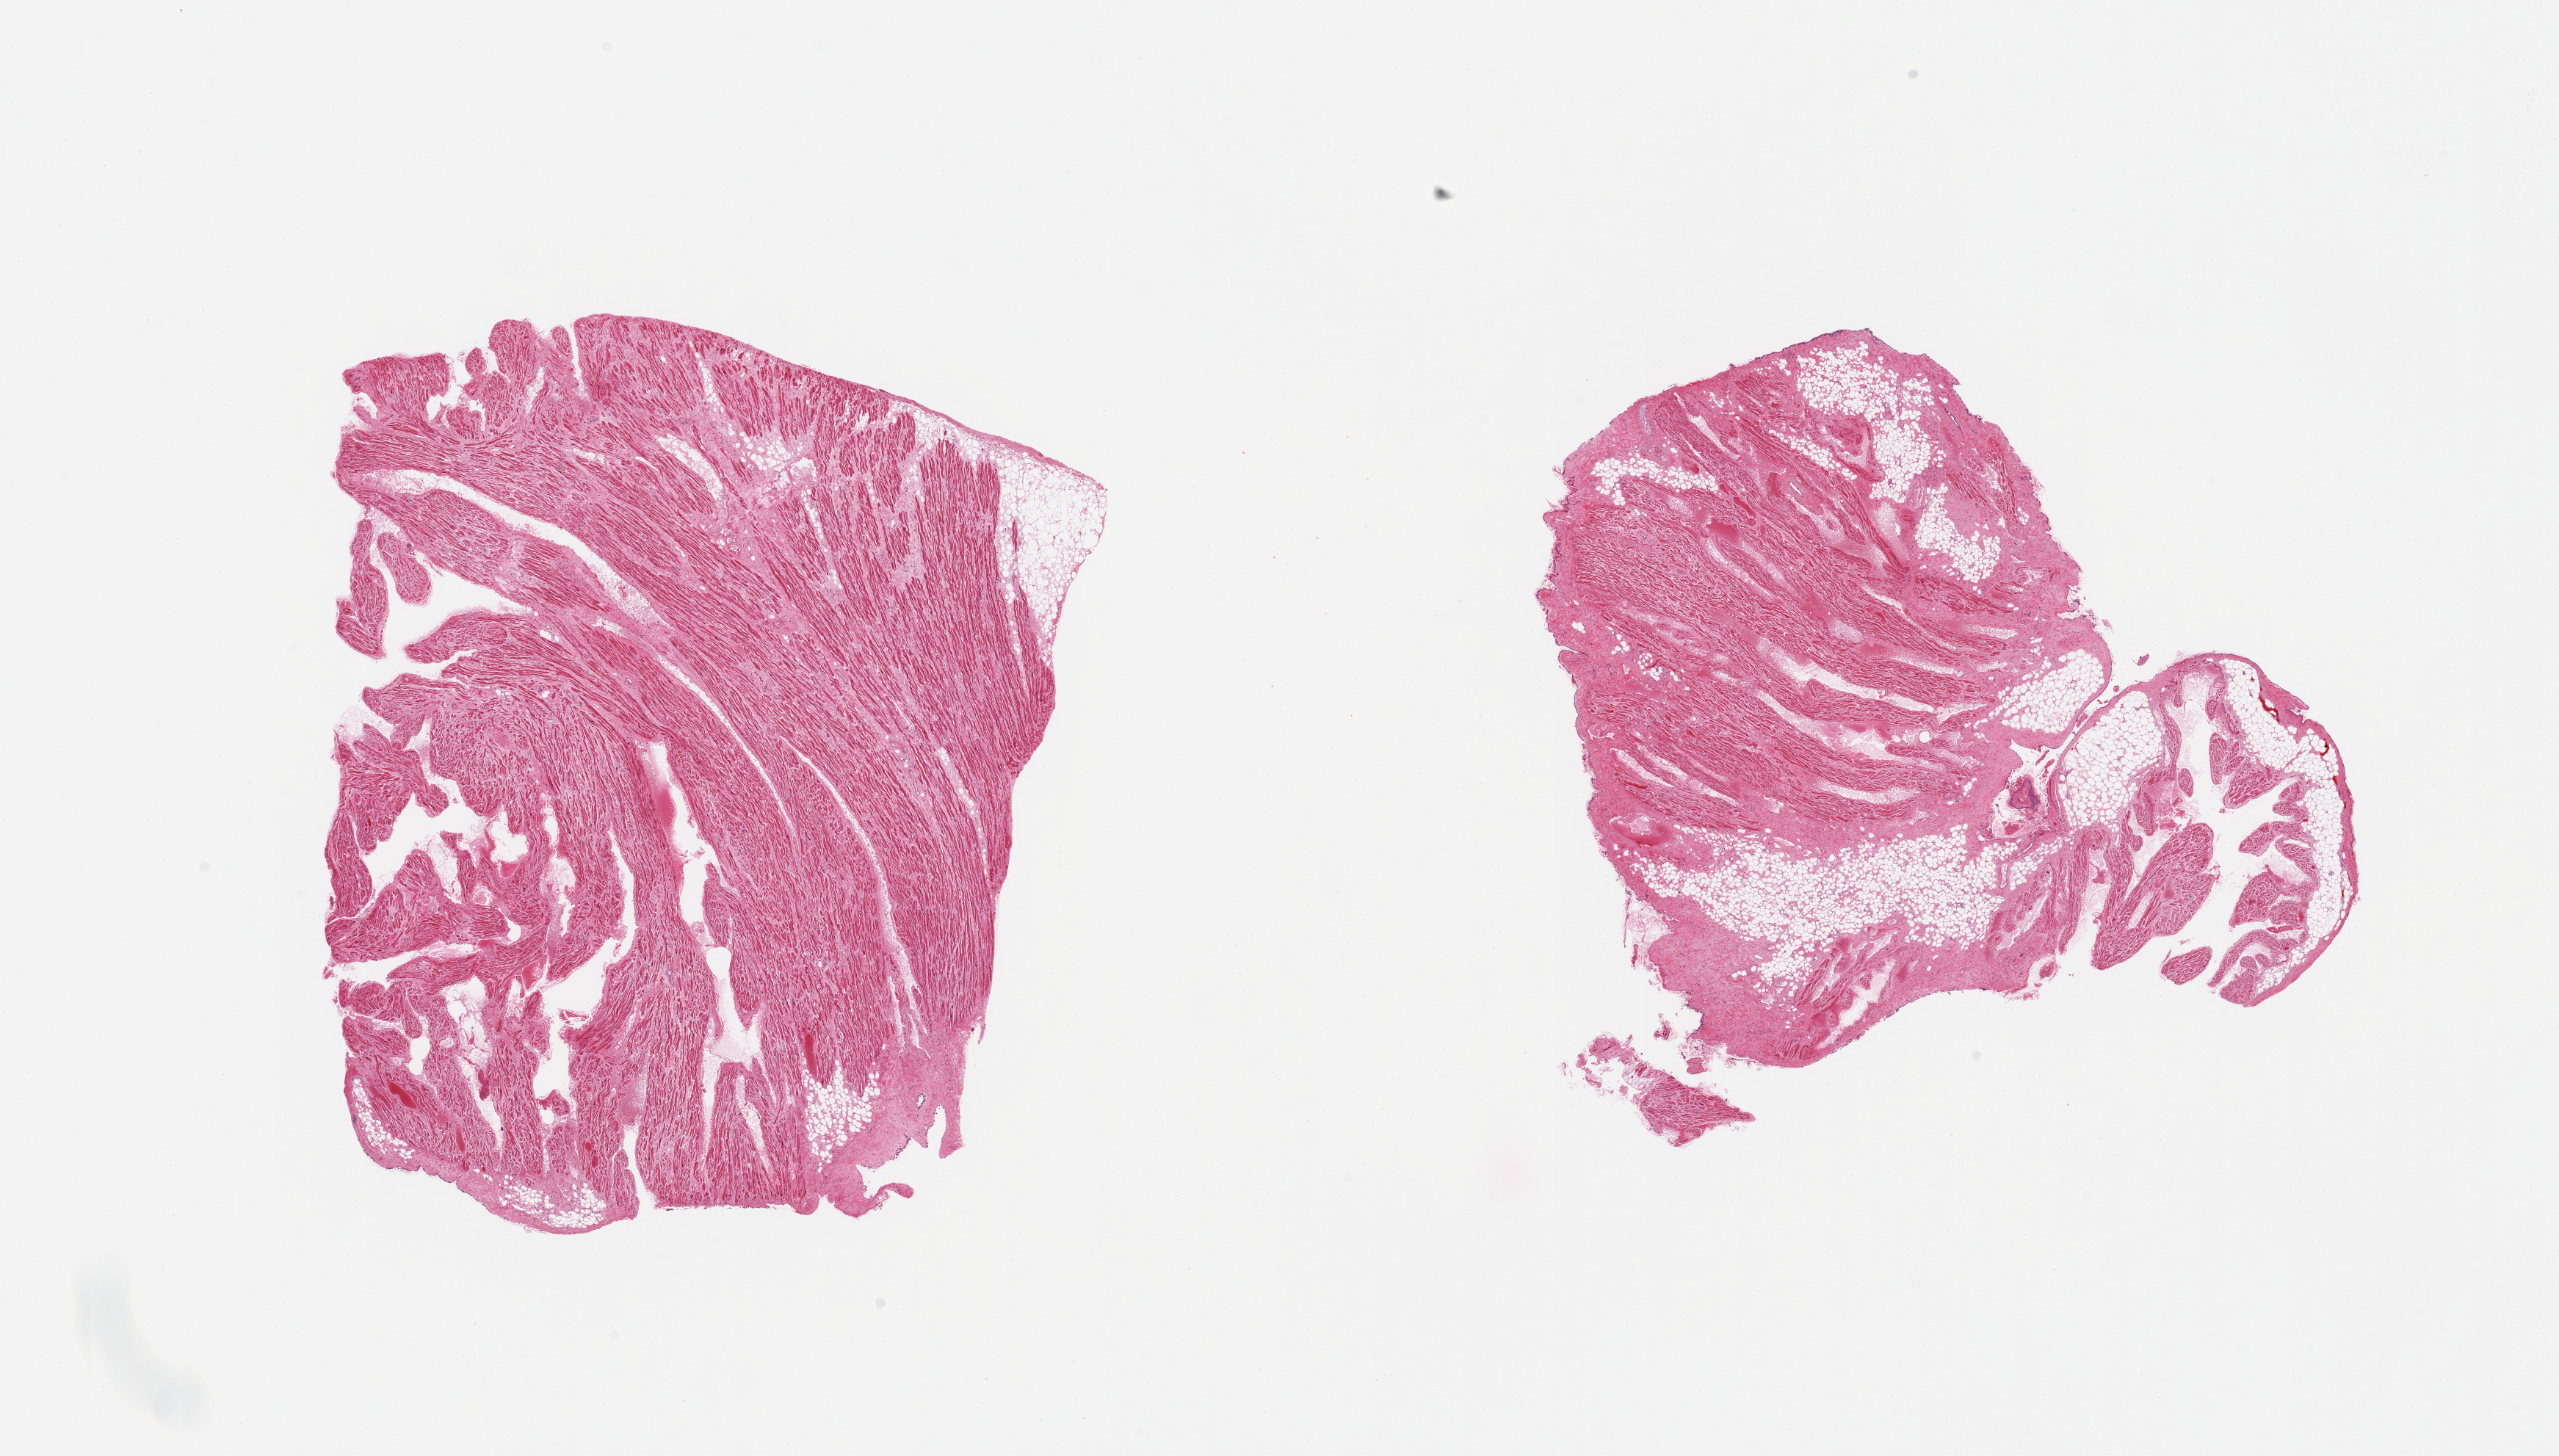
Whole-slide image, H&E stain, brightfield — whole scanned area (about 27.6 x 15.7 mm, acquisition: 20x scan) shown as a low-resolution overview; PAXgene-fixed paraffin-embedded (PFPE) section; sampled site (target tissue): auricular appendage; tissue donor sample. Male donor.
Pathologist's review note for this sample: 2 pieces, interstitial fibrosis, one piece is up to ~40% fat/fibrosis.